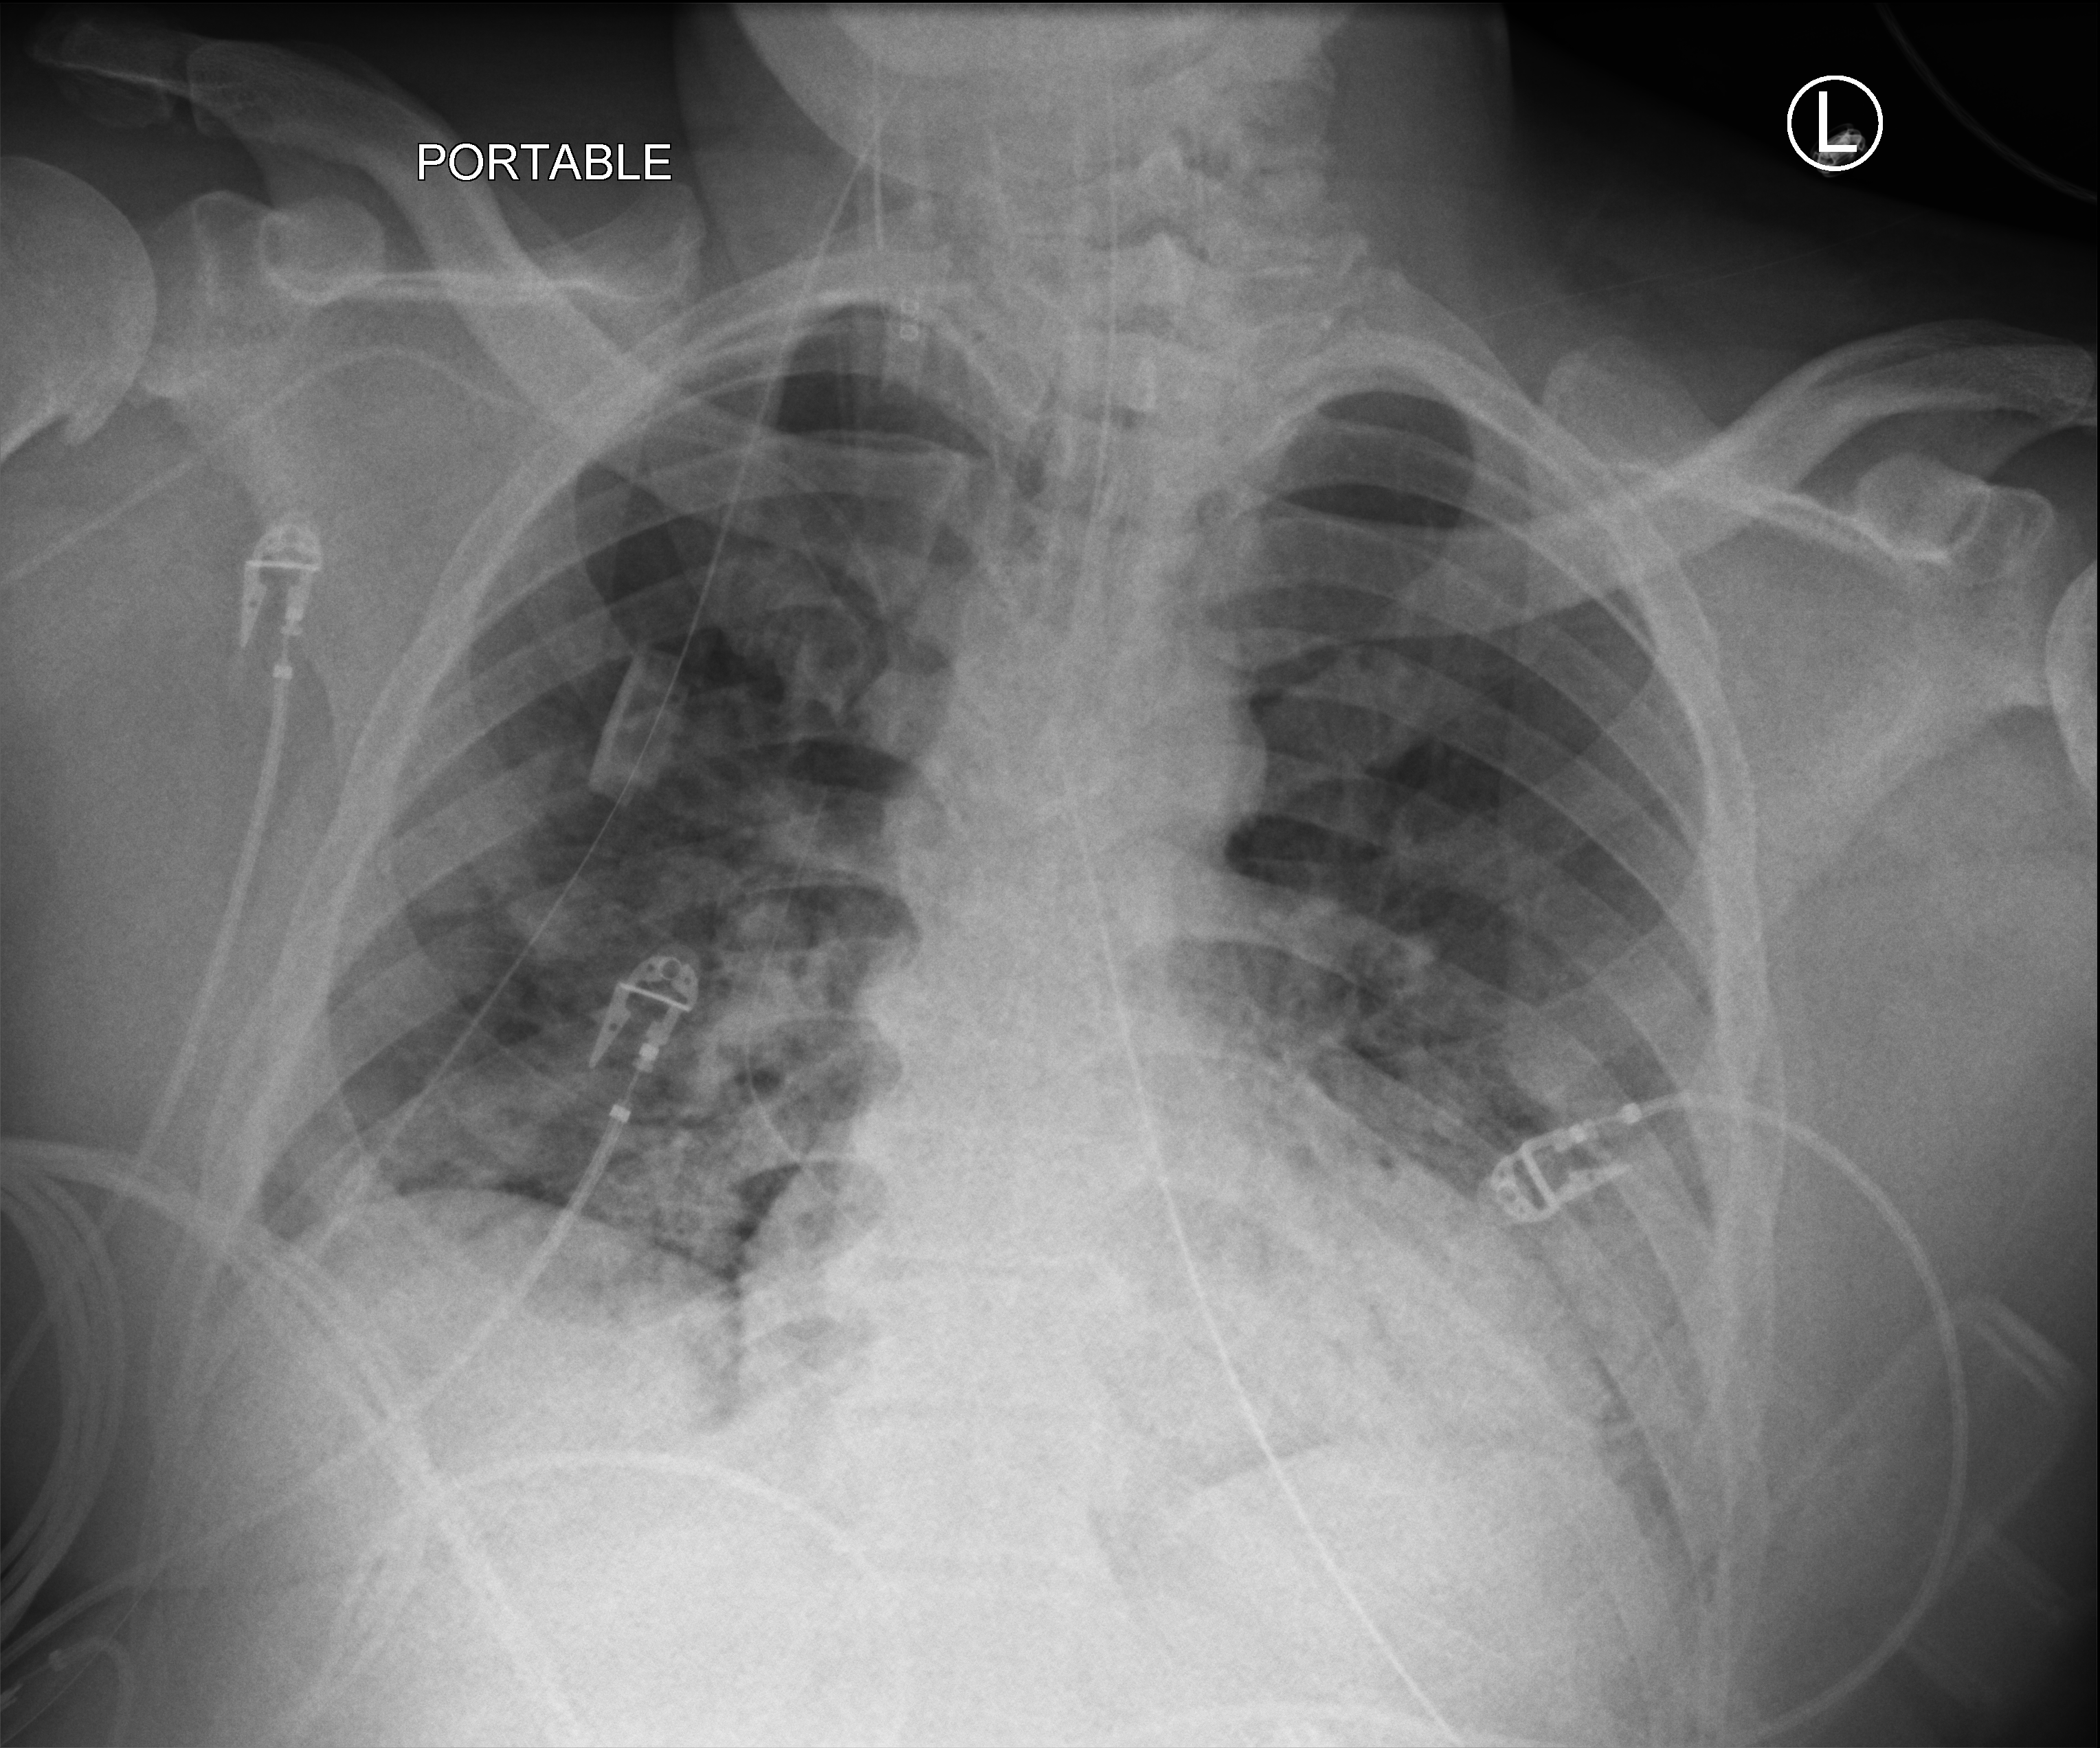
Chest X-ray (portable), anteroposterior (AP) projection. Patient hospitalised with COVID-19; male, aged 18–59 years.
Admission-level facts for this patient (not findings on this image; timing relative to this image not recorded): length of hospital stay: 41 days; mechanically ventilated during this hospital stay: yes.